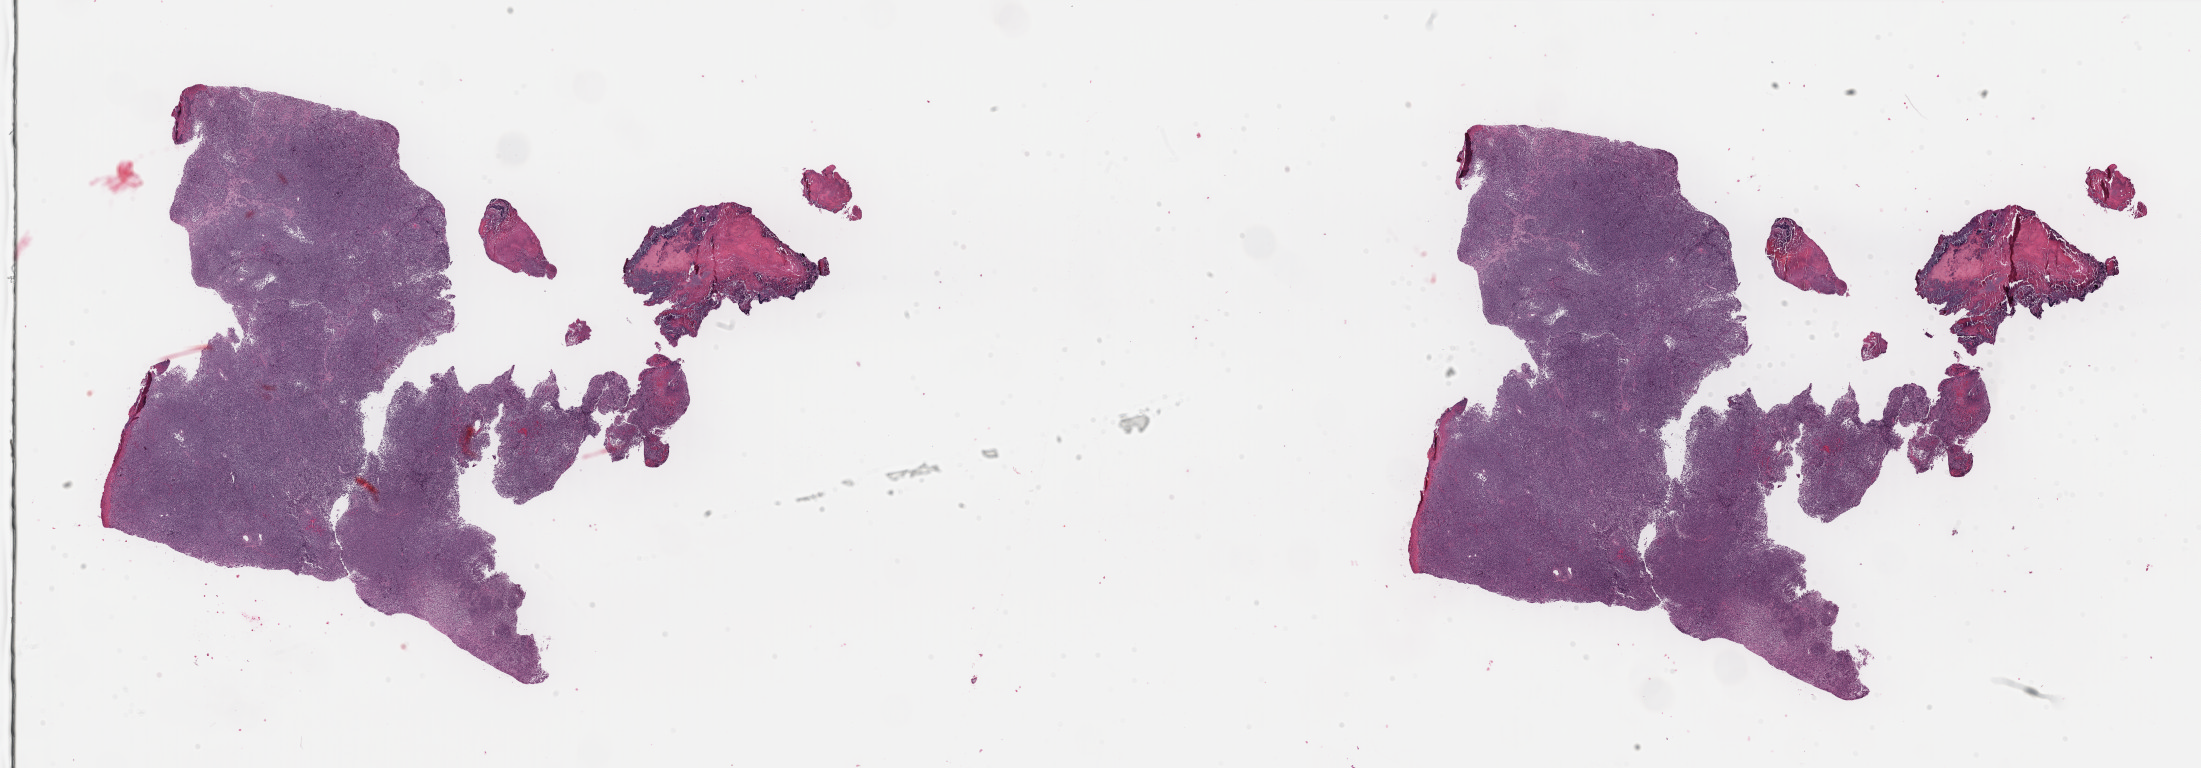
Digitized H&E tissue section (whole slide) — a low-resolution overview of the entire scanned area, about 34.8 x 12.2 mm (from a 40x scan); formalin-fixed paraffin-embedded (FFPE) diagnostic section; skin, primary tumour sample. Male patient.
* AJCC pathologic stage: IIC
* pathologic diagnosis: Lentigo maligna melanoma